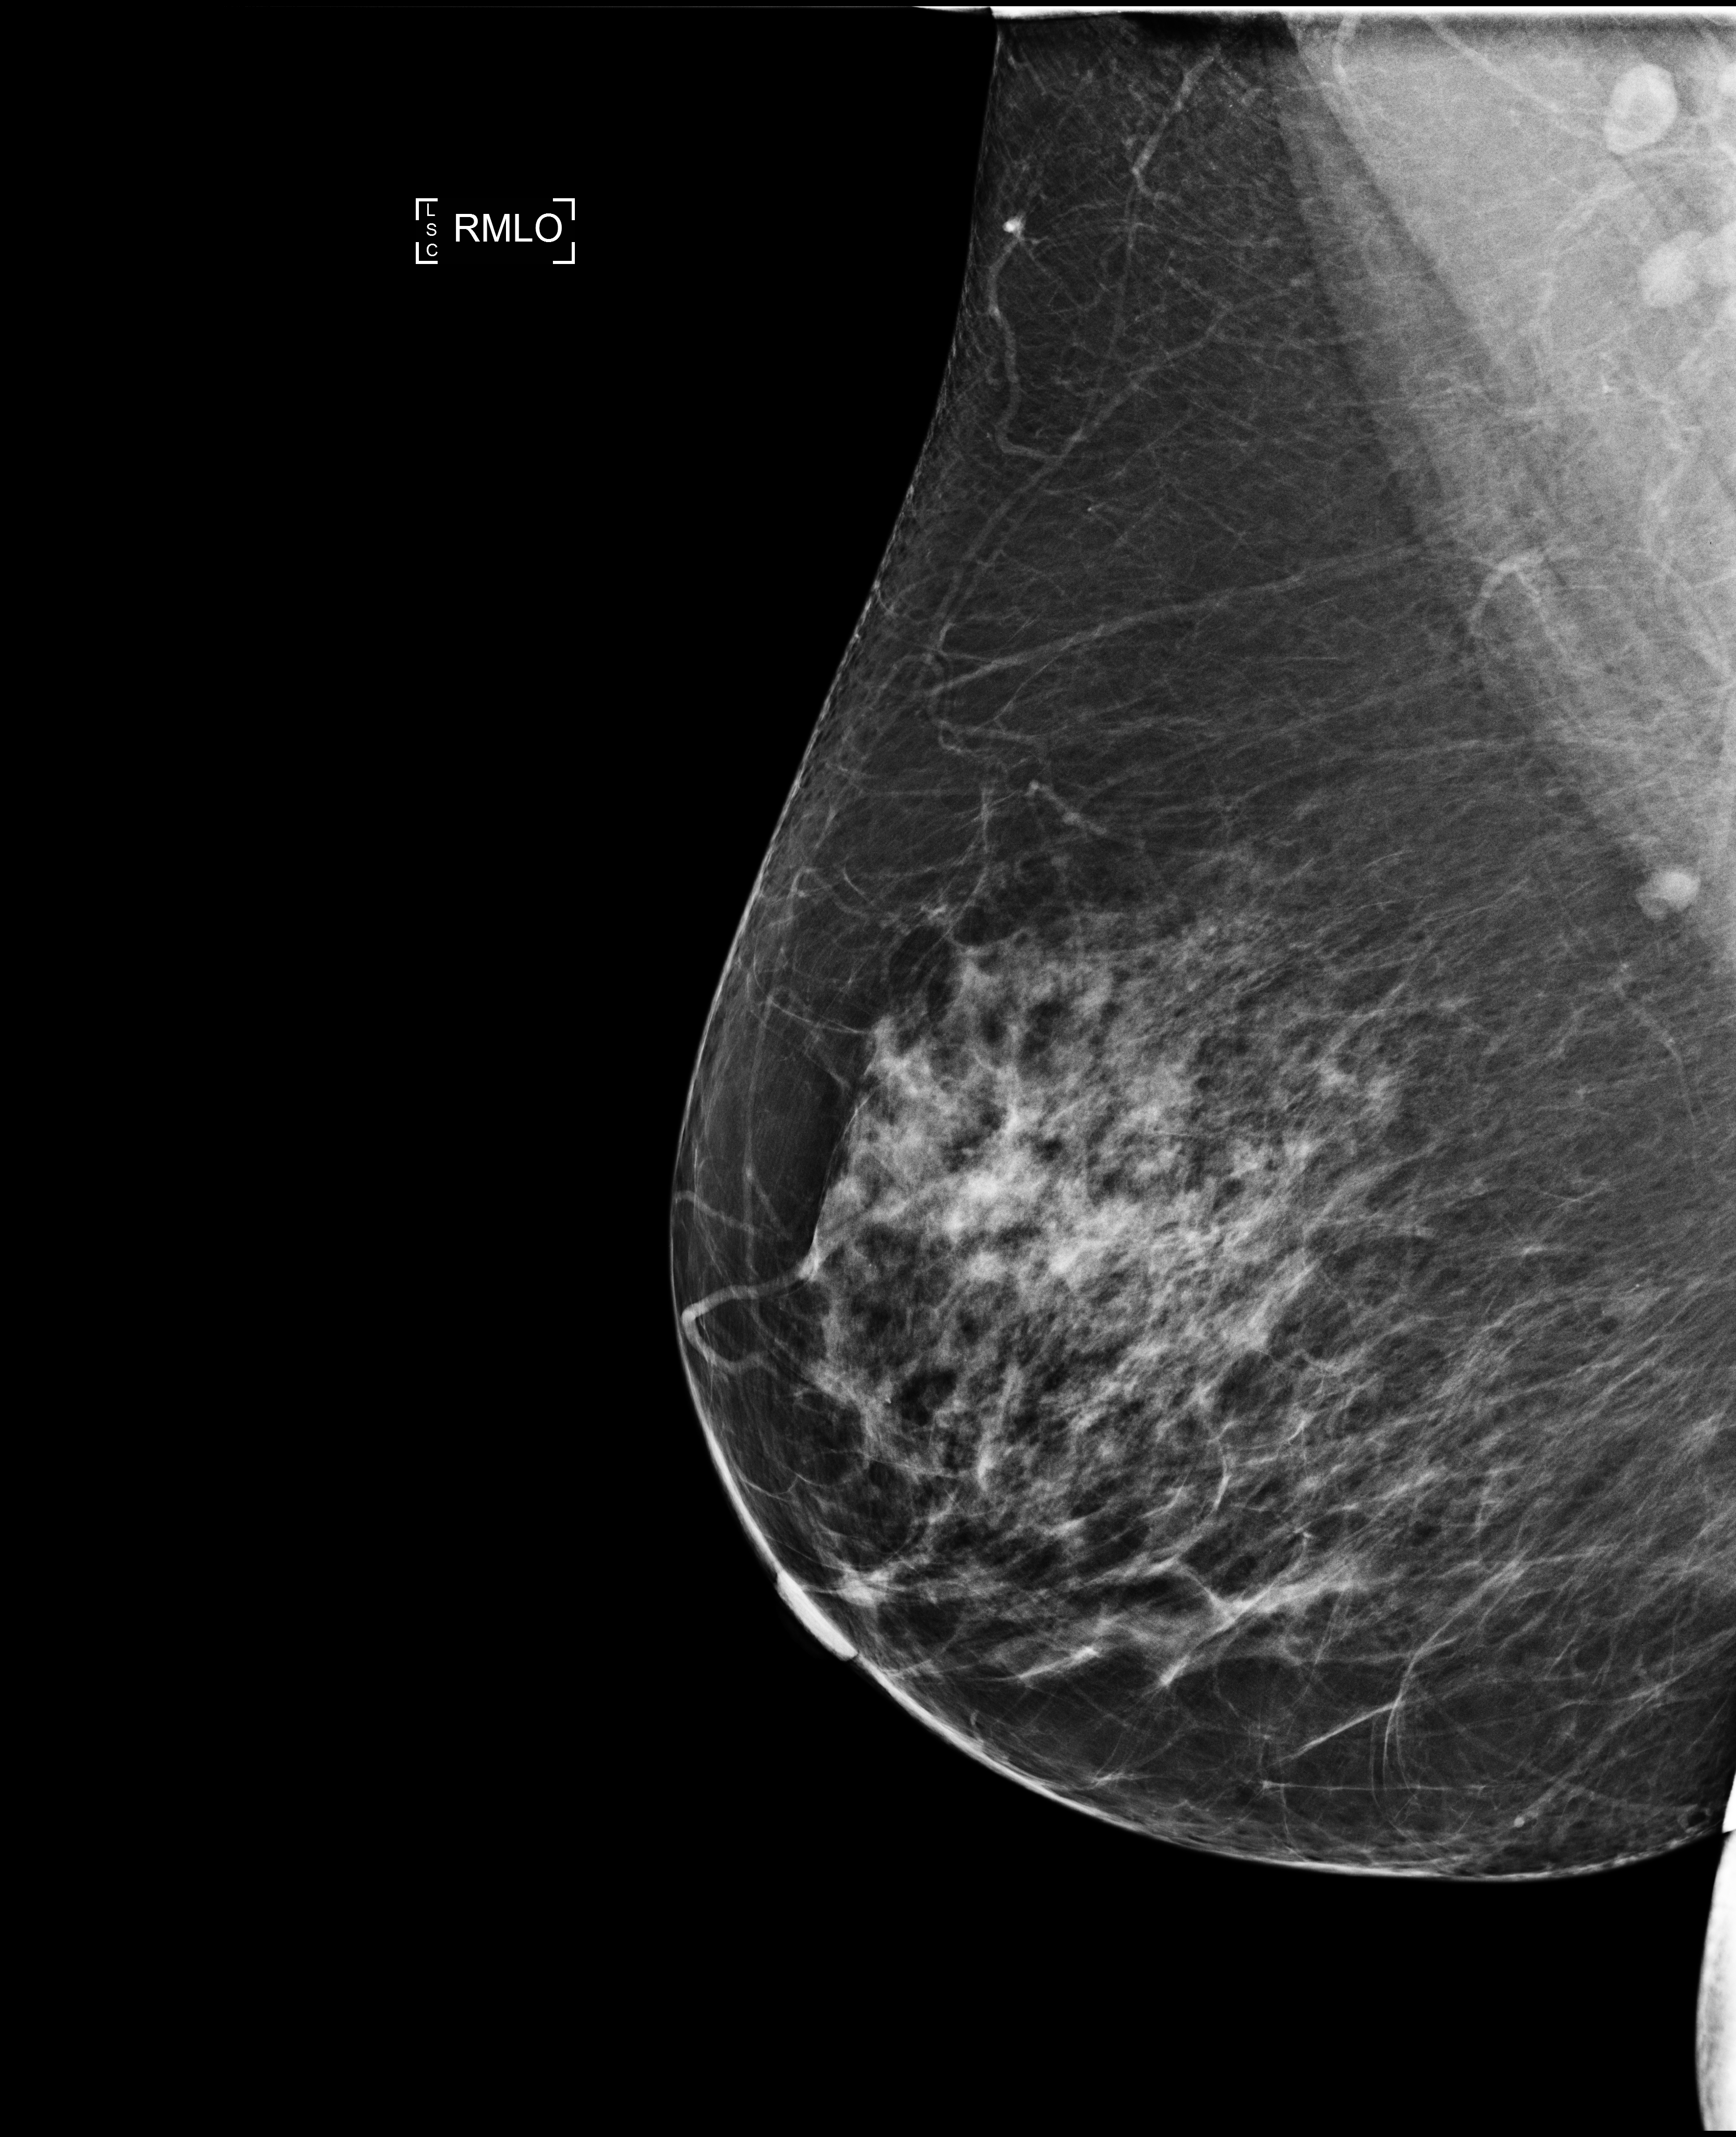
Digital mammogram (FFDM); right breast; MLO view; annual screening mammography examination; system: Selenia Dimensions. Patient: female, 57 years.
Breast density at the screening exam (both breasts): heterogeneously dense (BI-RADS density category c). Final BI-RADS assessment for this screening round (tomosynthesis exam, both breasts): category 2. Recall: no recall after this screen.